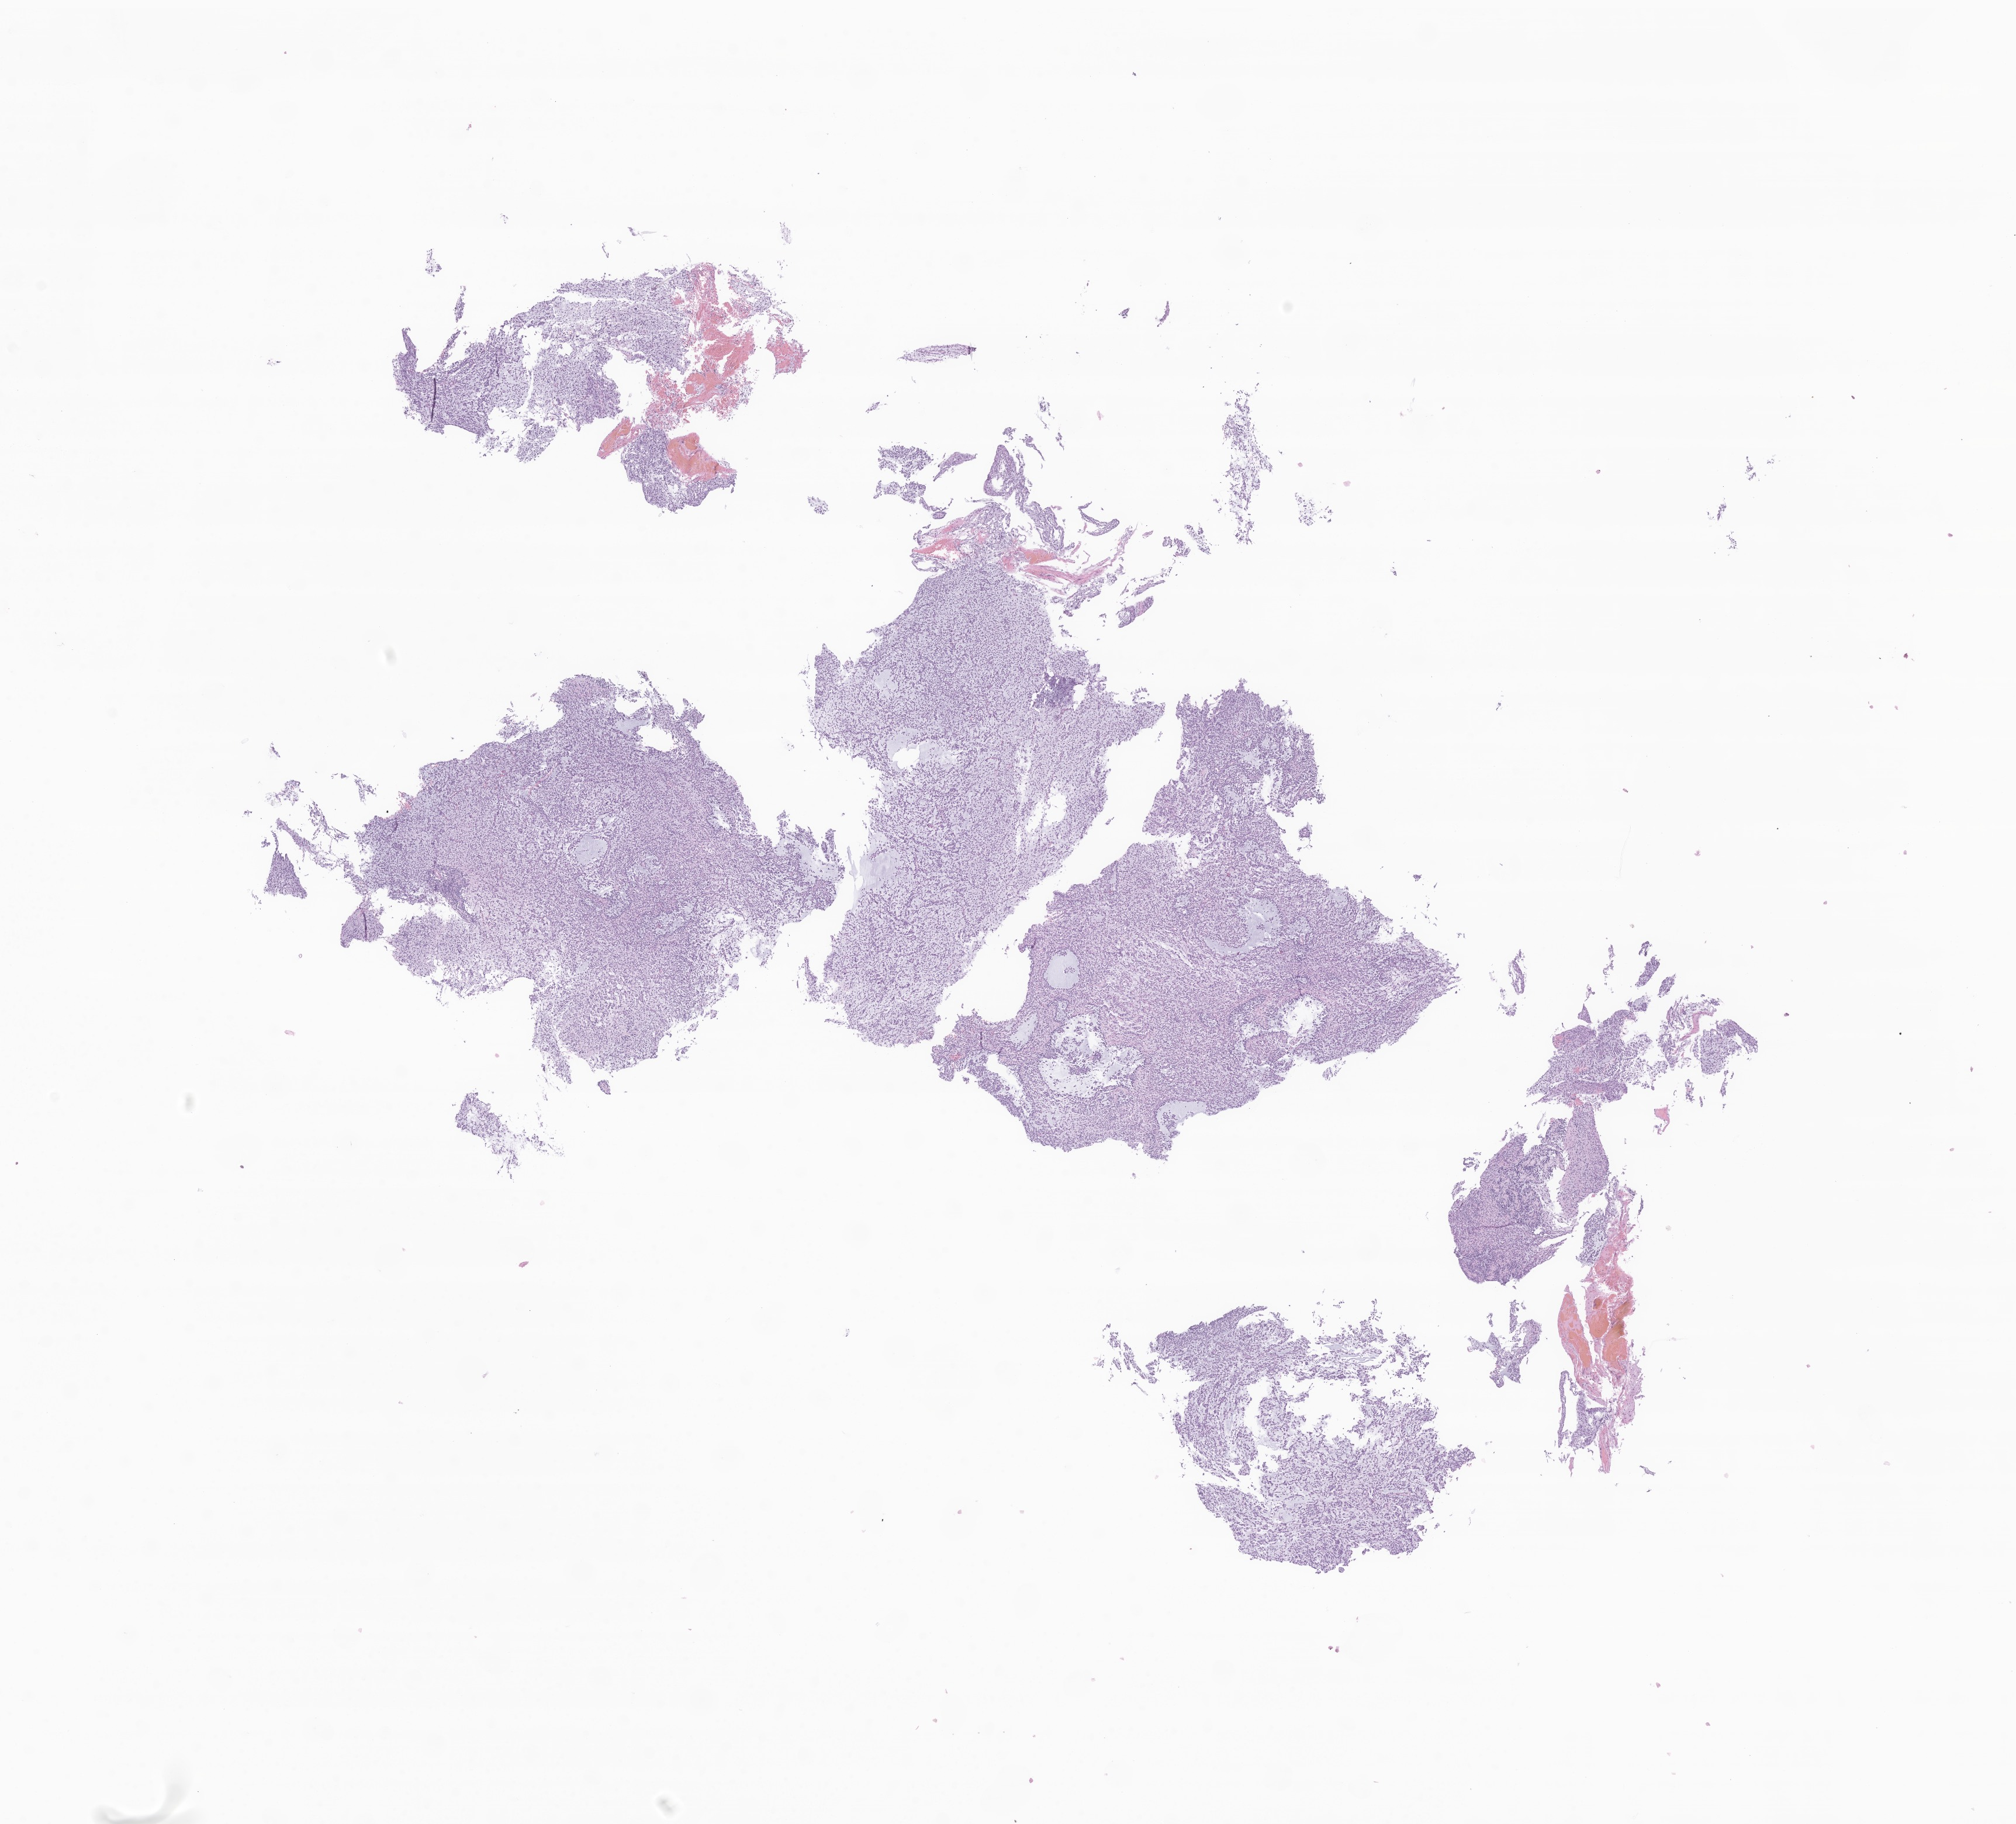
Digitized haematoxylin and eosin-stained section of tumor tissue from the temporal lobe — low-resolution overview of the scanned area, about 14.5 x 13.2 mm, formalin-fixed paraffin-embedded section. Female patient, age 215 months (17 years 11 months).
* recorded diagnosis: Neoplasm, uncertain whether benign or malignant